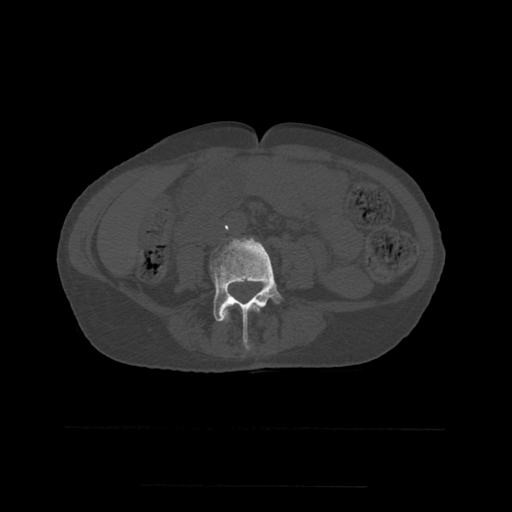
CT including the spine, one axial slice. Position 170 of 544 along the scan axis. Bone window (W 1800 / L 400 HU). 1.25 mm slice thickness. 512 × 512 image matrix, field of view 350 × 350 mm. Patient age 58 years. From the clinical record (not read from this slice): primary cancer: lung.
Structures marked on this image (semi-automatically segmented with operator editing):
- L3 vertebra: bounding box <222,304,260,322> (left, top, right, bottom; pixels)
- L4 vertebra: <210,237,283,350>